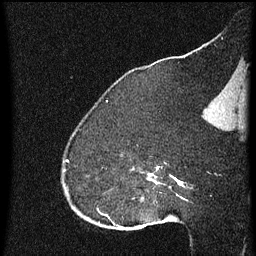
Breast MRI (dynamic contrast-enhanced), one sagittal slice. Slice 46 of 60 in the series (ordered by position). Dynamic contrast-enhanced series, image 2 of 4 at this slice position (ordered by acquisition). 1.5 T. TE 4.2 ms, TR 8 ms. 2 mm slice thickness. 256 × 256 image matrix. Female patient, age 52 years.
Outlined on this slice (semi-automatic segmentation, software-assisted and operator-edited):
- analysis volume of interest (the breast-tissue region the enhancement analysis was run in; not a lesion): box from (x=73, y=152) to (x=172, y=219) px
- tumour enhancement mask (voxels above the 70 % enhancement threshold inside the analysis volume of interest): (x=150, y=168)–(x=172, y=185)